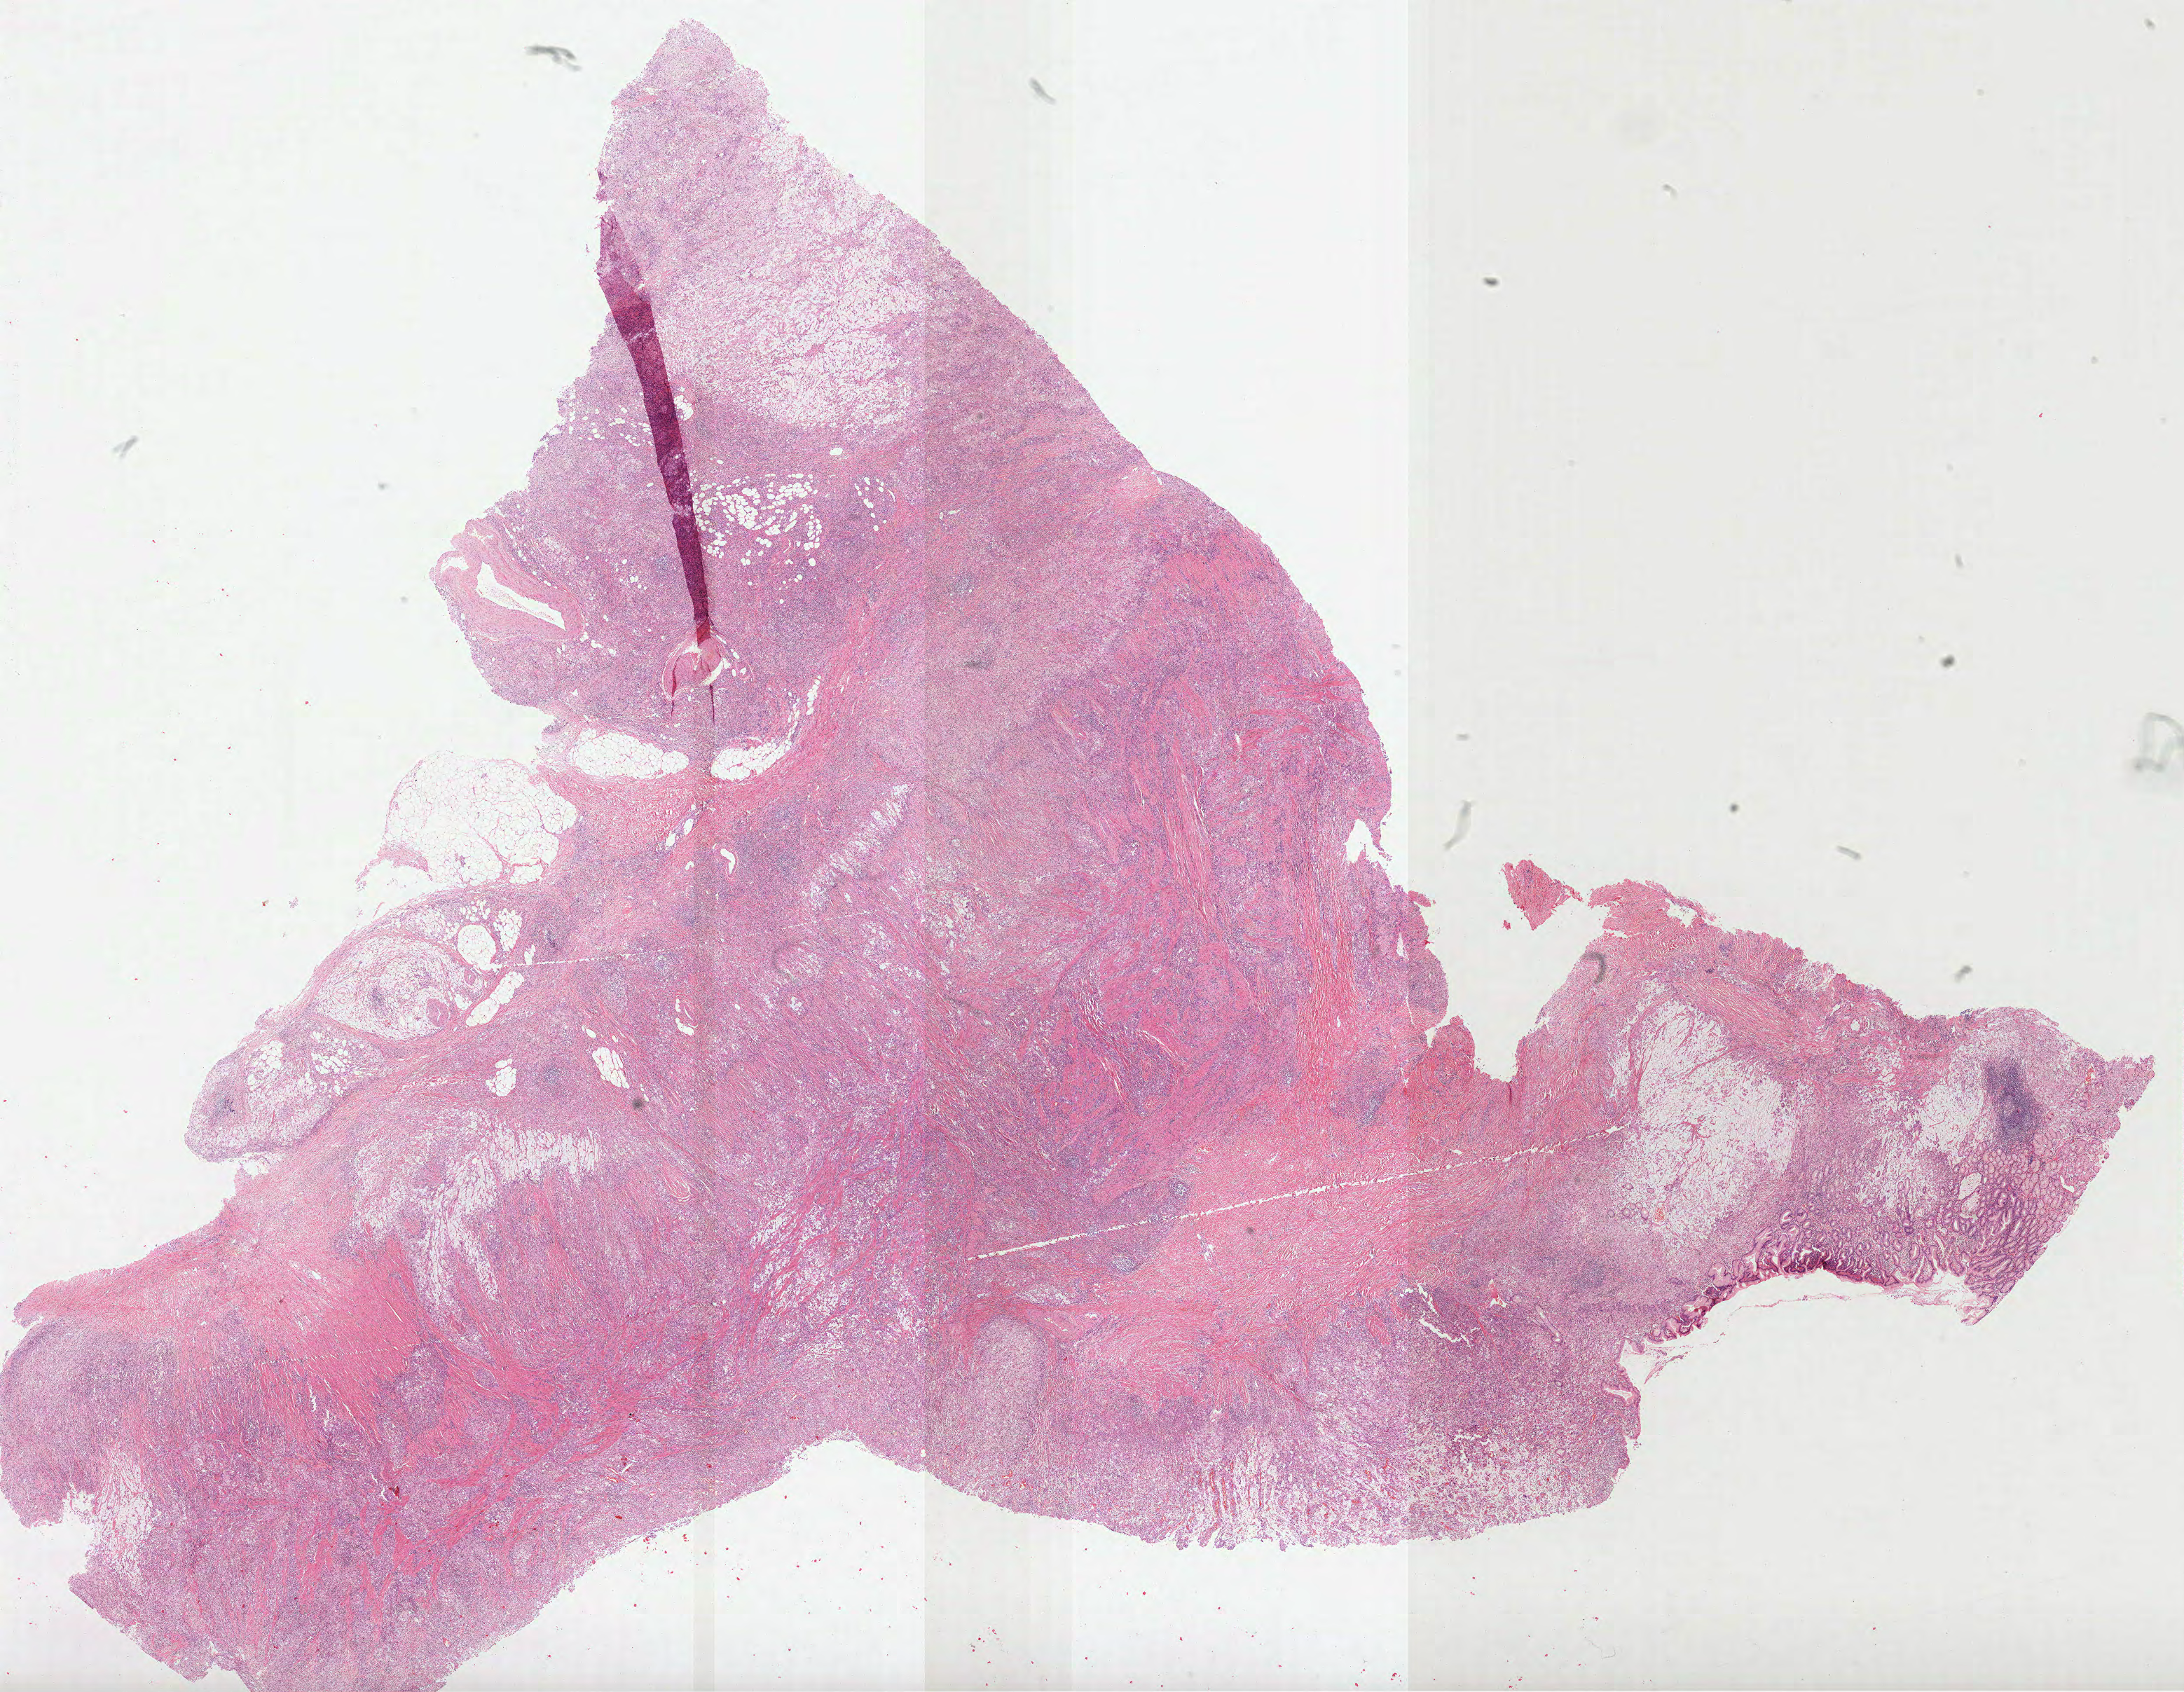
Digitized H&E-stained tissue section (whole slide) — shown as a low-resolution overview of the whole scanned area (about 25.1 x 19.5 mm); formalin-fixed paraffin-embedded (FFPE) diagnostic section; sample: primary tumour, stomach. Male patient; age at initial diagnosis 64 years. Histologic grade: G3 (poorly differentiated).
Pathologic diagnosis: Adenocarcinoma, NOS (cardia, NOS). AJCC pathologic stage: IIIB (7th edition). Lymph nodes positive (case pathology): 9 of 15 examined.